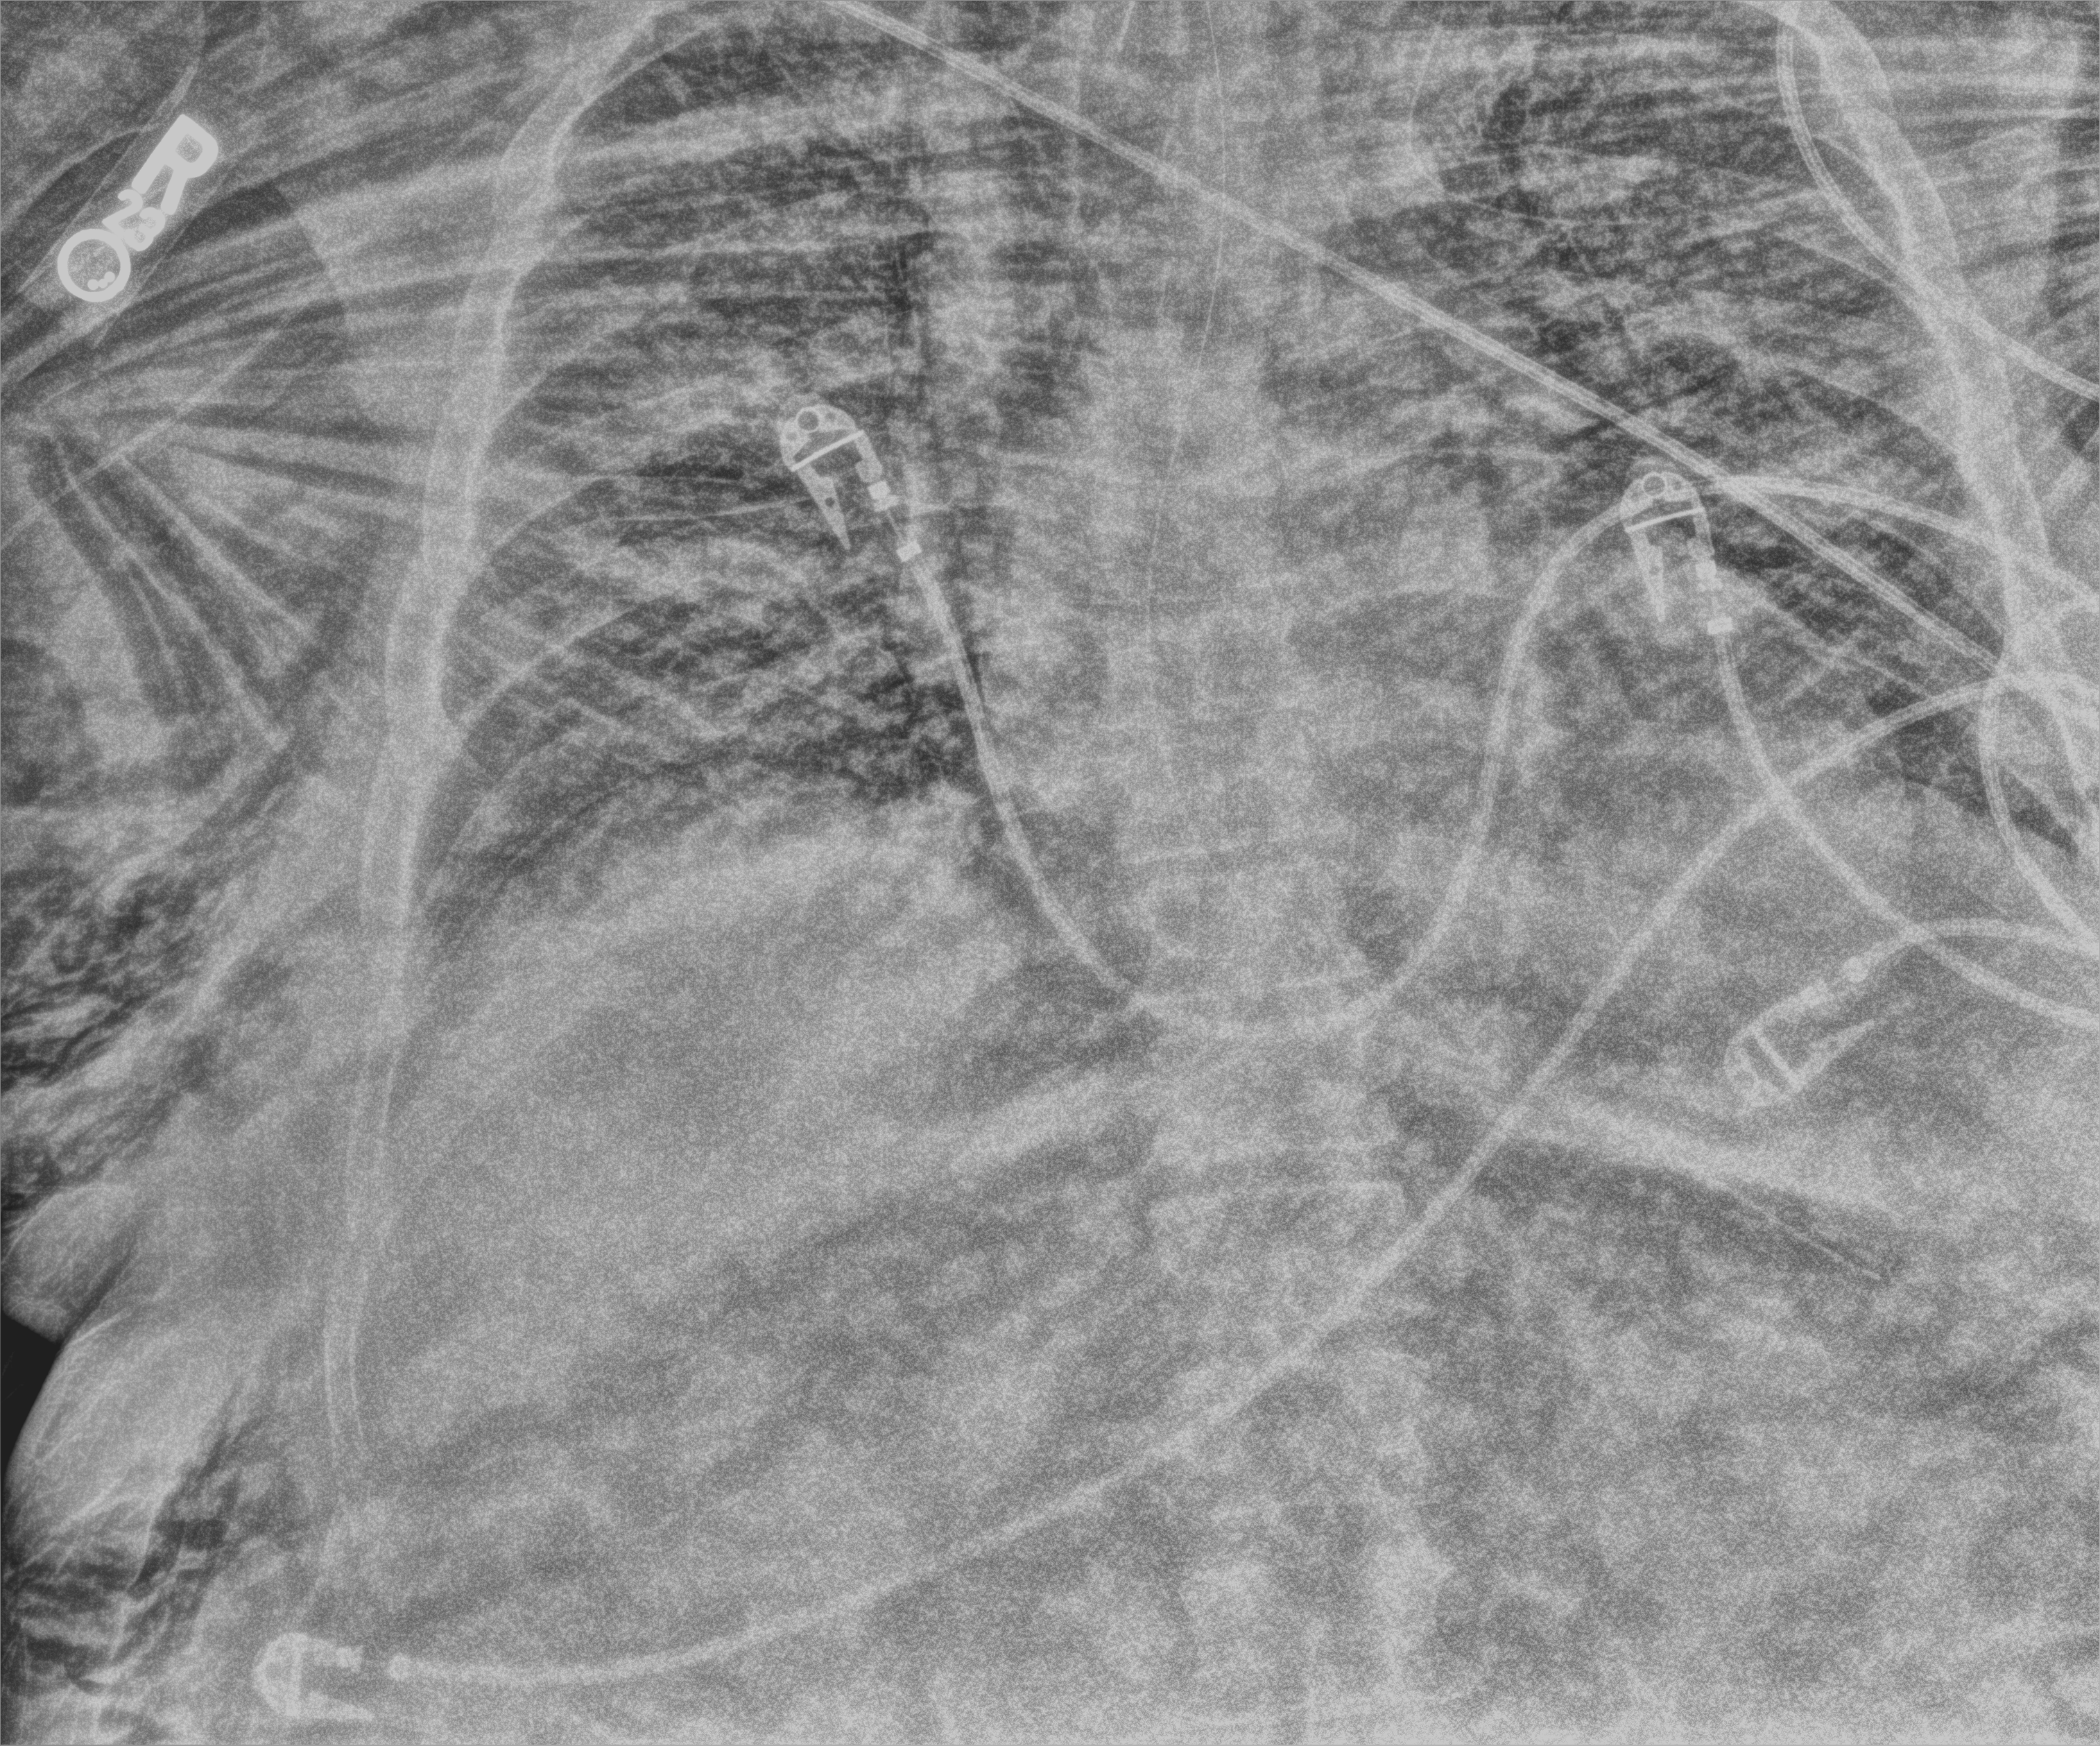
Bedside chest radiograph (computed radiography); anteroposterior (AP) projection. Adult patient hospitalised with COVID-19, age 18–59 years.
From the hospital-stay record, not from the radiograph (when in the stay this image was taken is not recorded): admitted to intensive care during this hospital stay: yes; mechanically ventilated during this hospital stay: yes; length of hospital stay: 26 days.